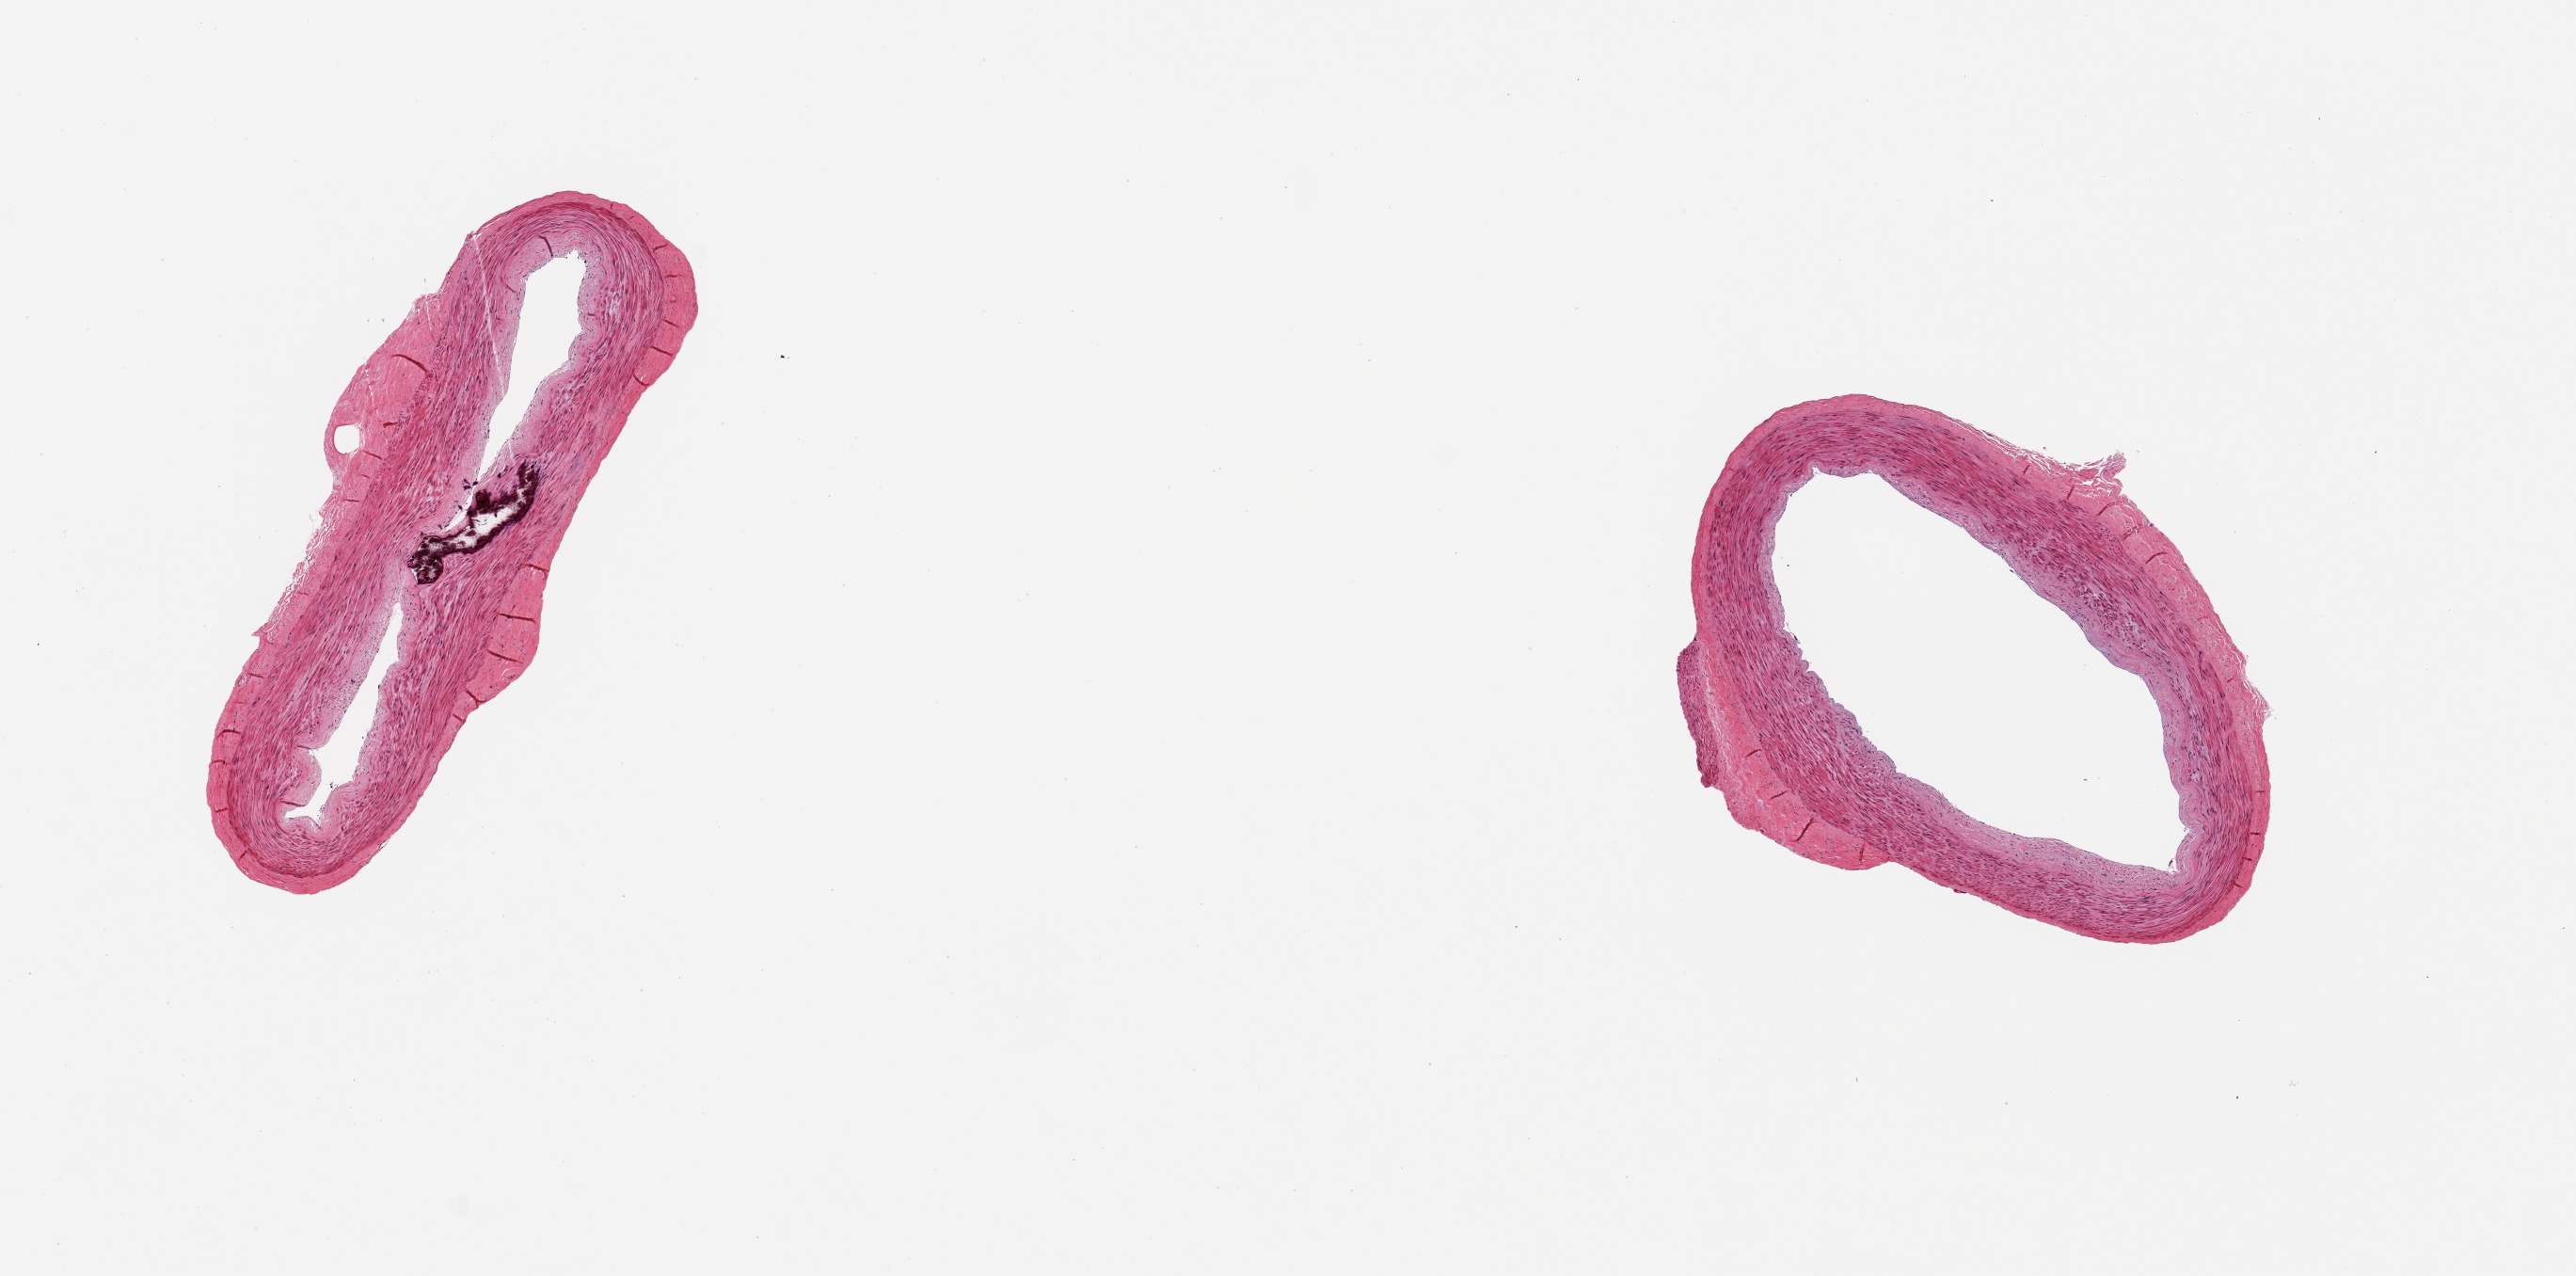
Hematoxylin and eosin (H&E) whole-slide image — a low-resolution overview of the entire scanned area, about 10.8 x 5.4 mm (from a 20x scan). Donor sex: male.
Specimen: PAXgene-fixed paraffin-embedded (PFPE) section; sampled site (target tissue): tibial artery; tissue donor sample.